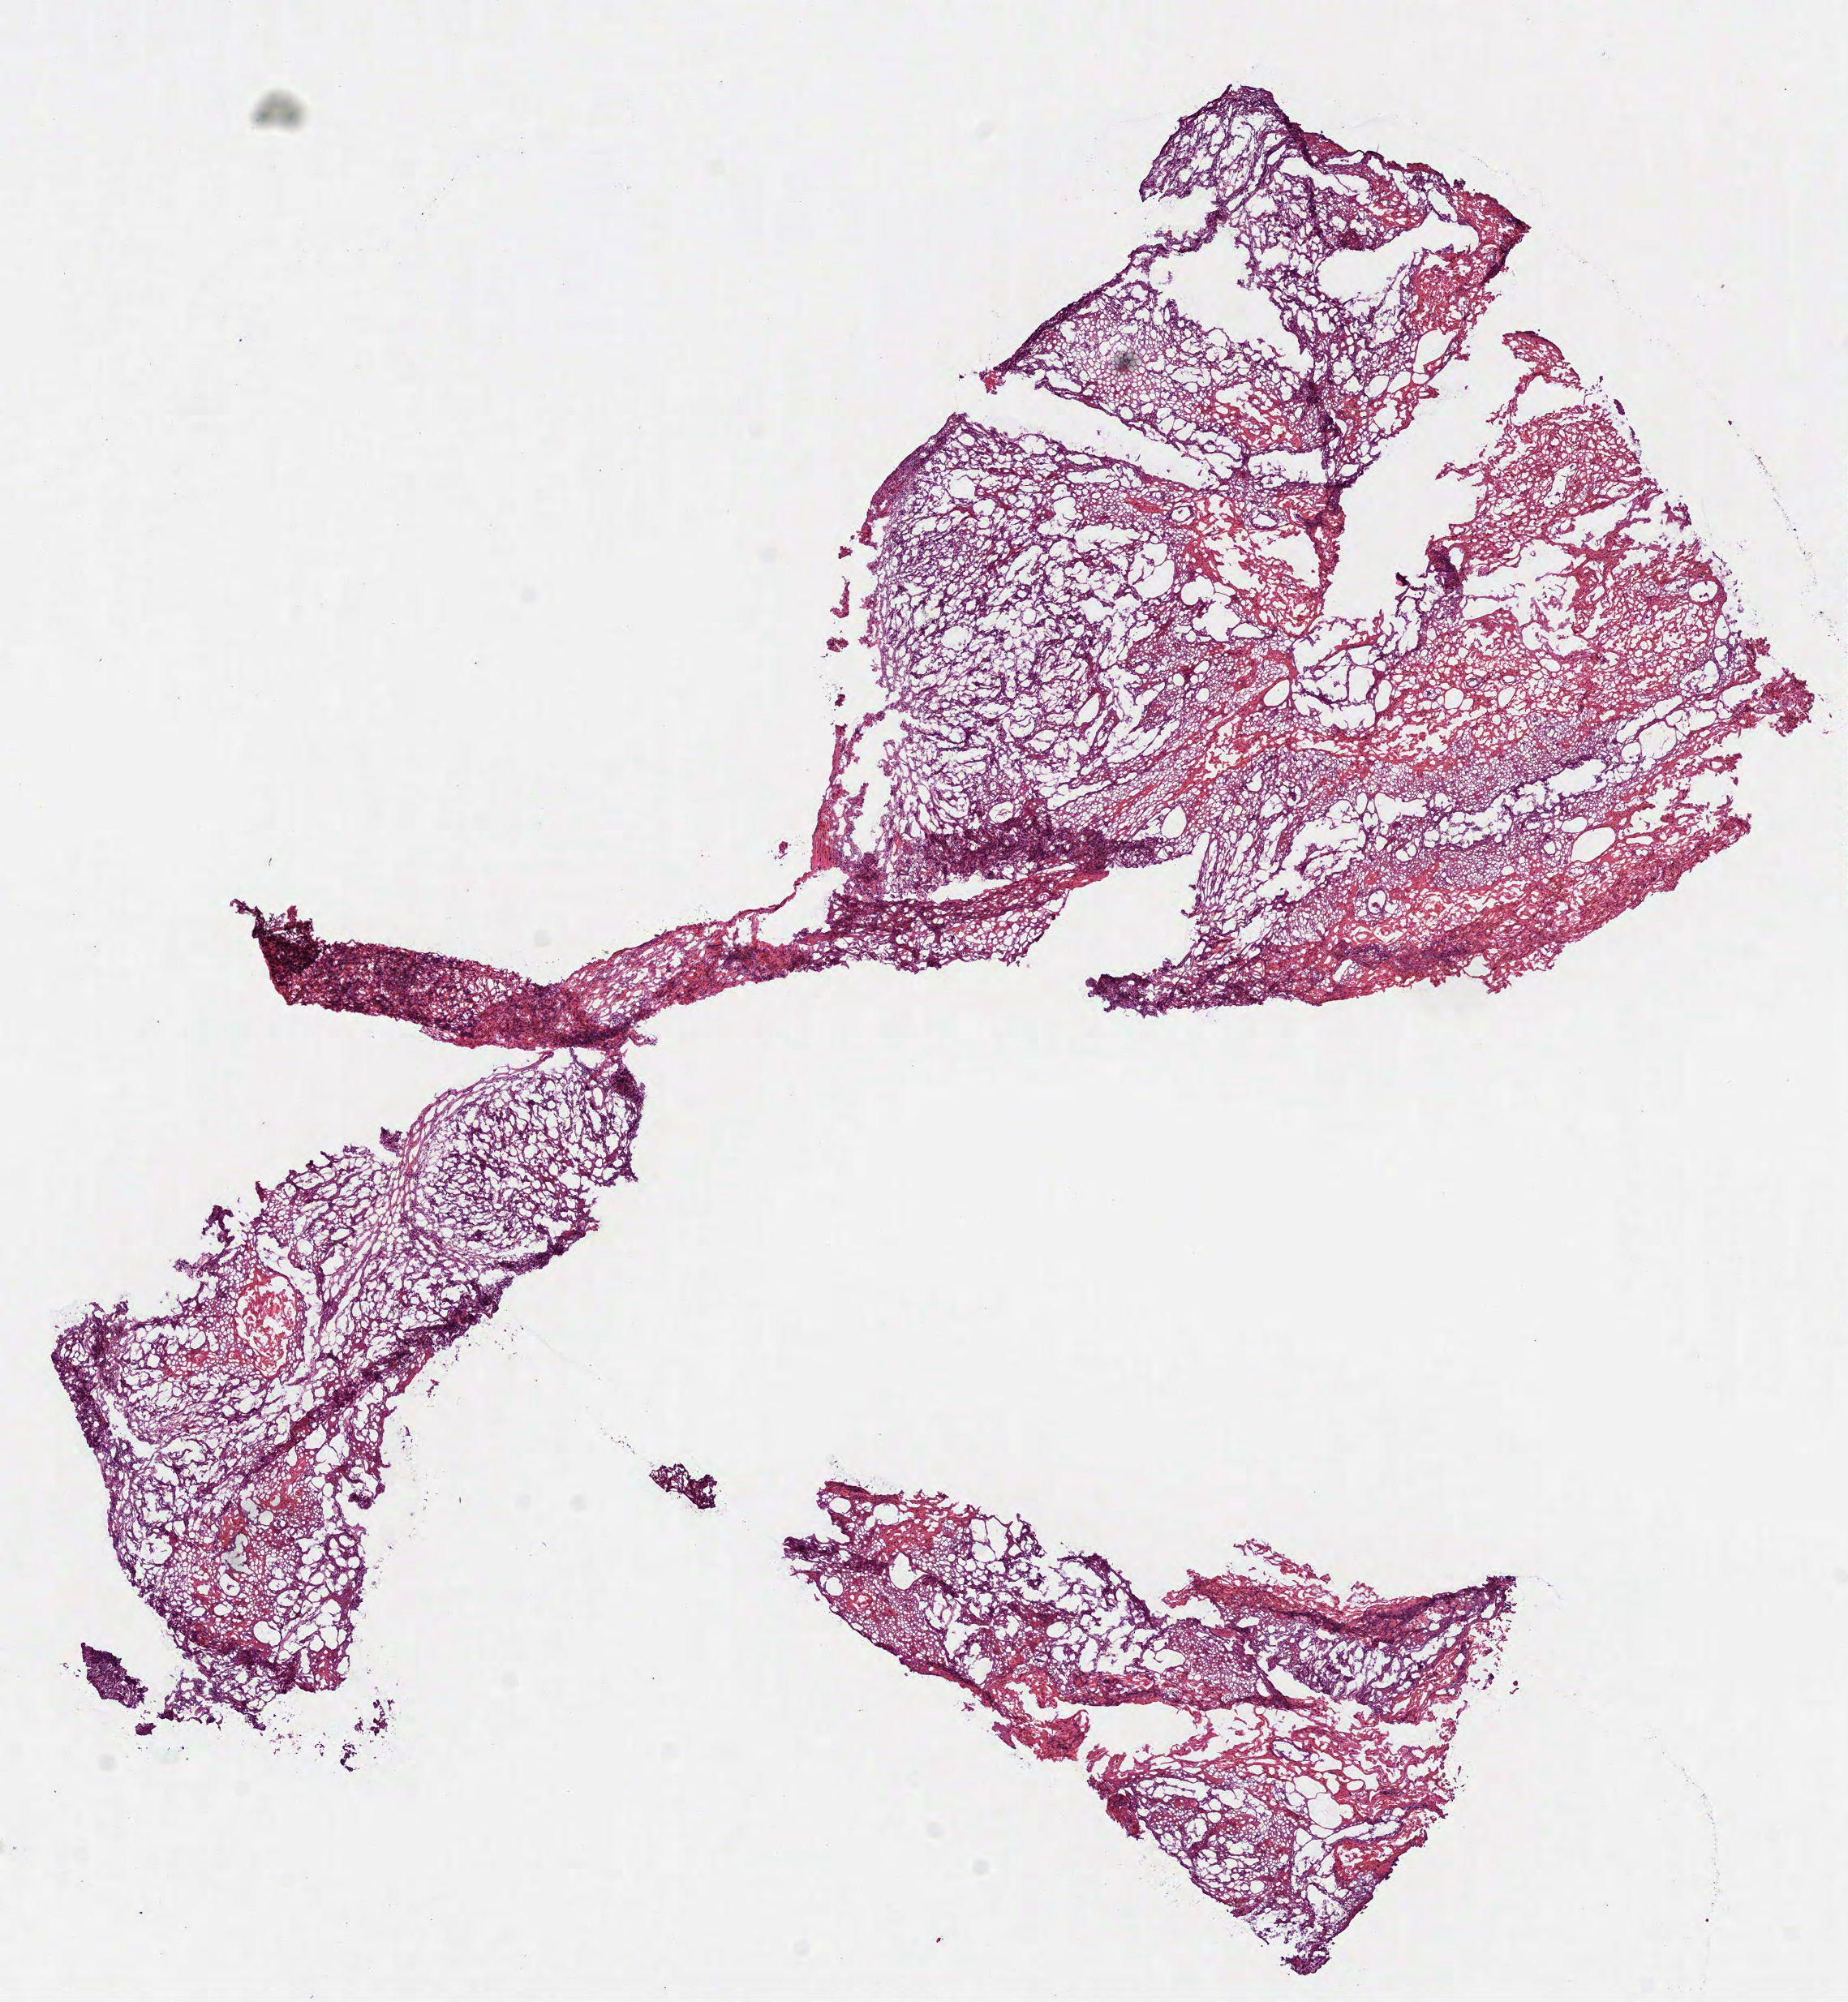
H&E-stained whole-slide image — shown as a low-resolution overview of the whole scanned area (about 9.2 x 10.0 mm, acquisition: 40x scan); frozen section from the top of the tissue portion; head and neck, primary tumour sample. Patient: male, age at initial diagnosis 59 years. Histologic grade: G2 (moderately differentiated). Composition of this section per pathologist review: tumour cells 85%, tumour nuclei 80%, normal cells 0%, stromal cells 0%, necrosis 15%. Inflammatory infiltration, as recorded: lymphocyte infiltration 2%, monocyte infiltration 0%, neutrophil infiltration 1%.
* AJCC pathologic stage: IVA
* pathologic diagnosis: Squamous cell carcinoma, NOS
* lymph nodes positive (case pathology): 0 of 22 examined